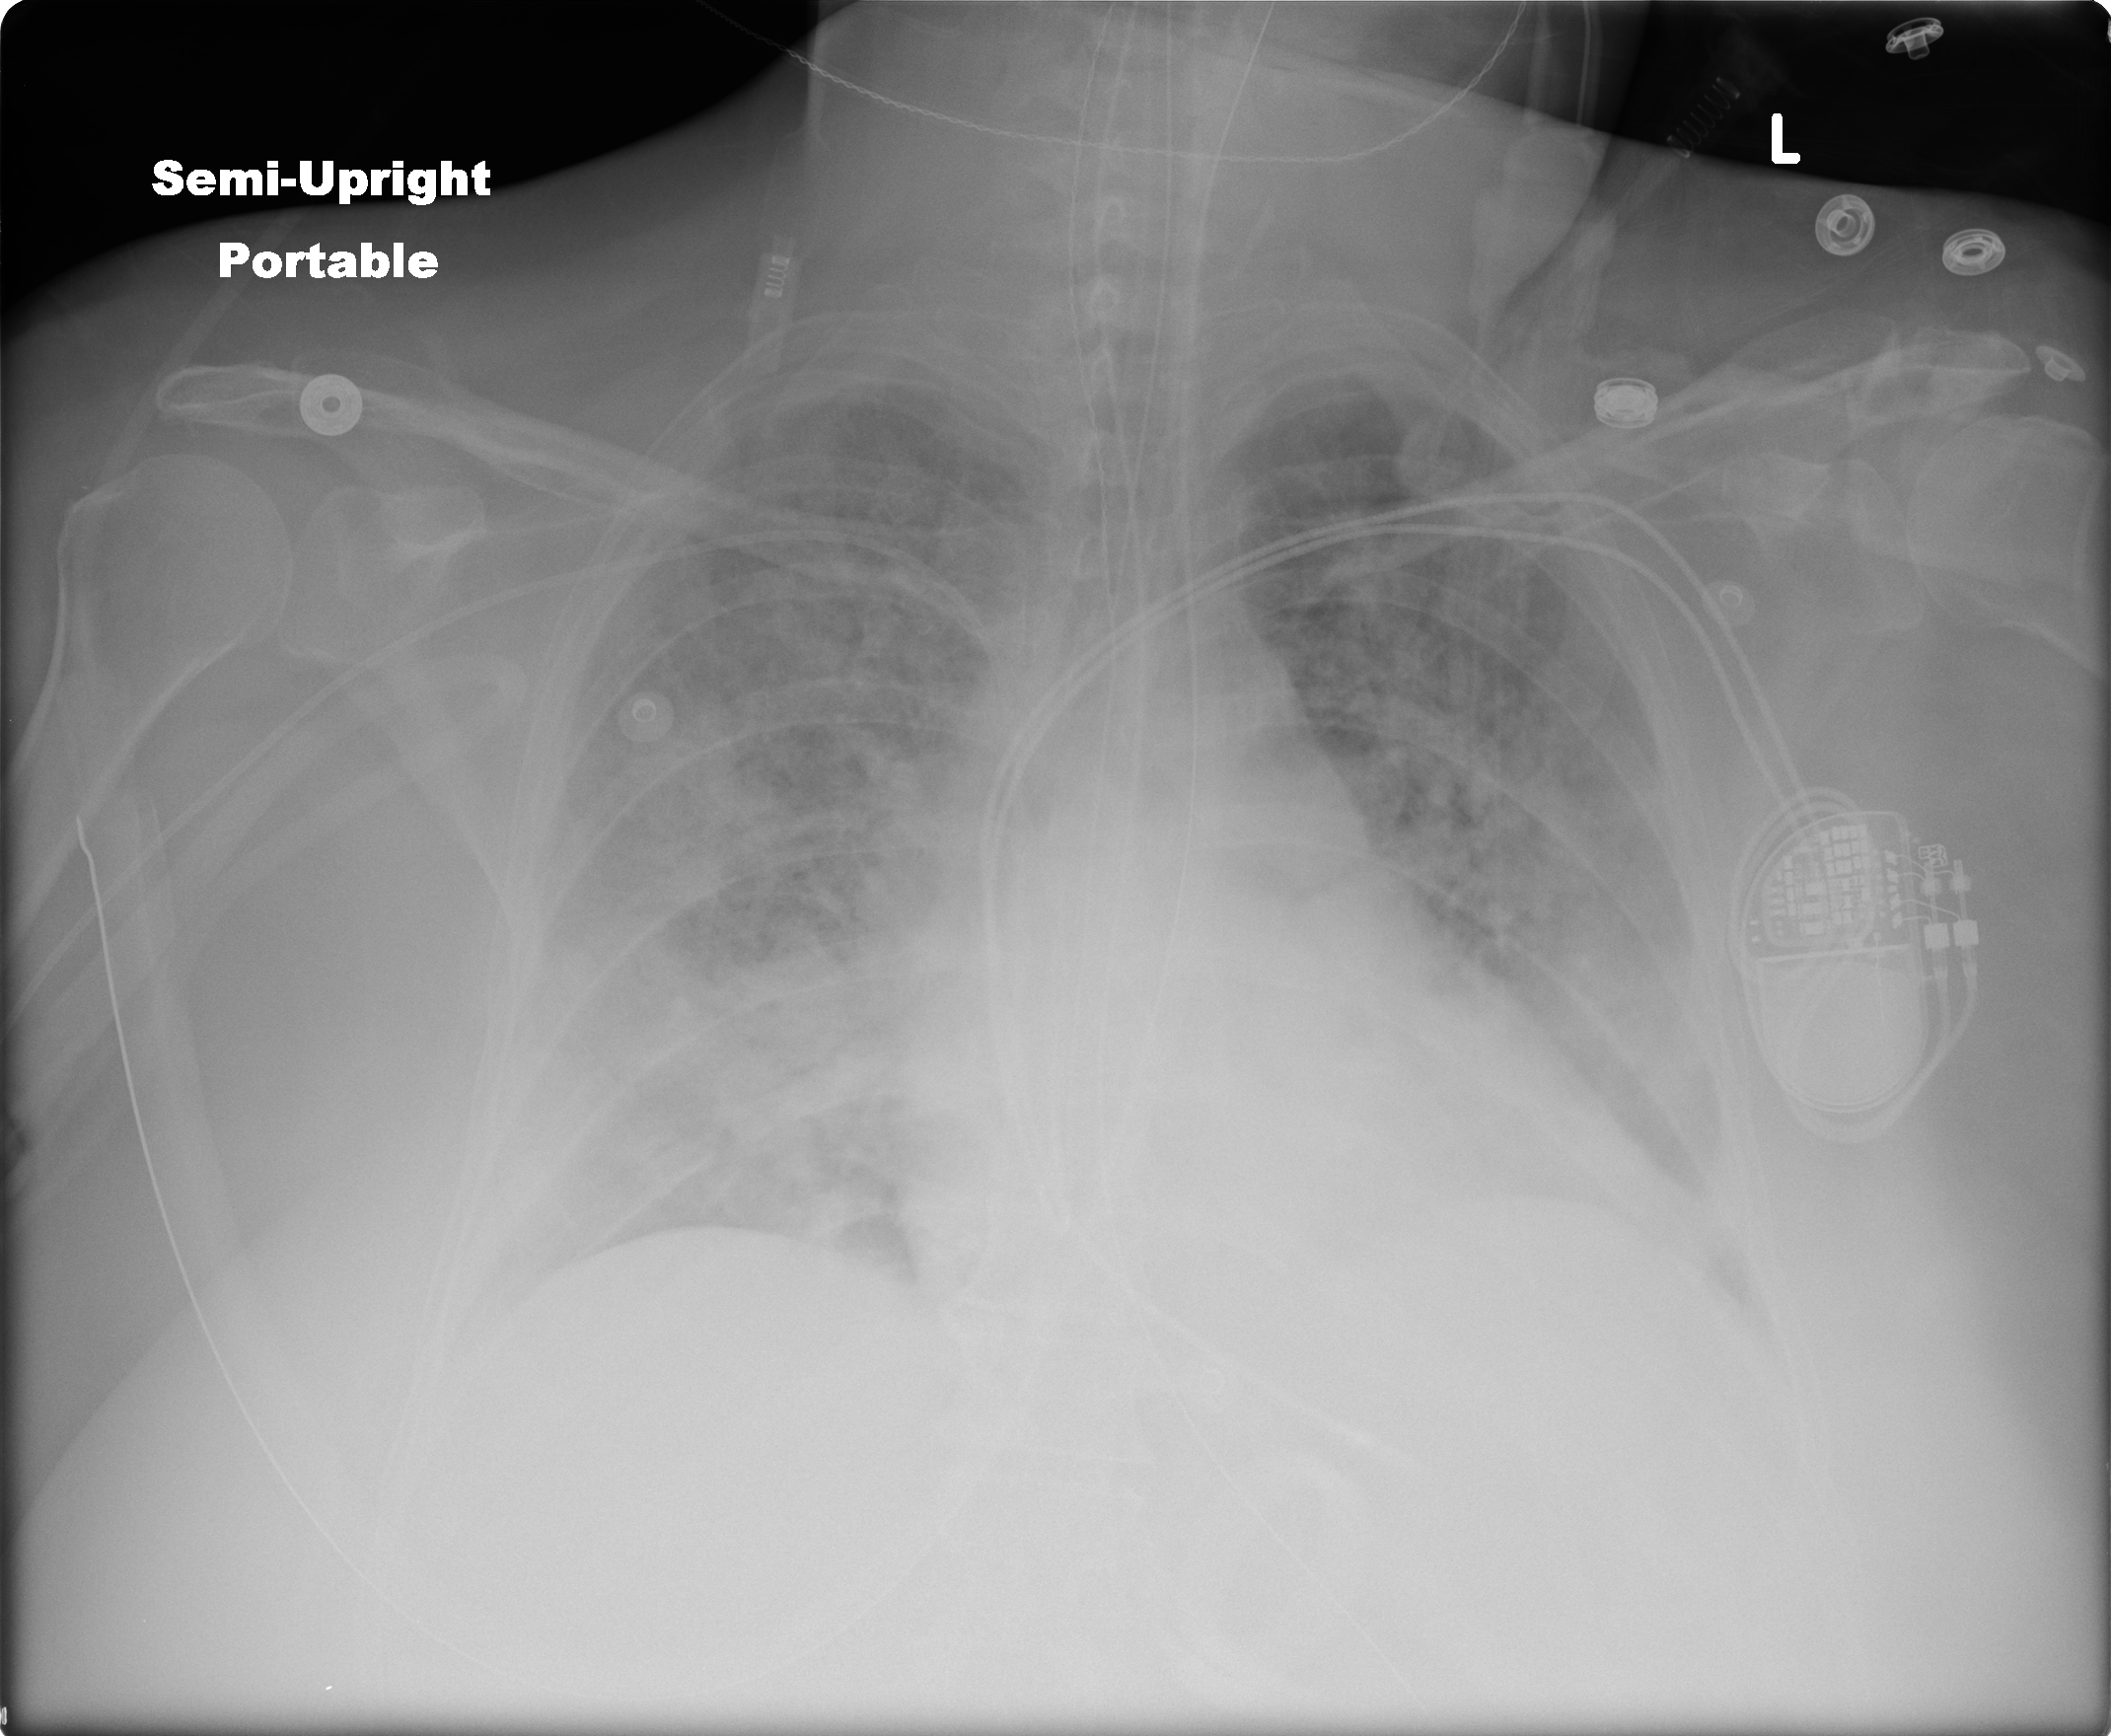
Chest X-ray (portable), AP projection. Female patient, age 57 years; imaged 3 days after the COVID-19 diagnosis.
Key findings recorded by the radiologist: interval worsening of diffuse bilateral multifocal pneumonia with diffuse haziness of both lungs consistent with the clinical concern for ARDS. Changes in the right are worse in comparison to the left.